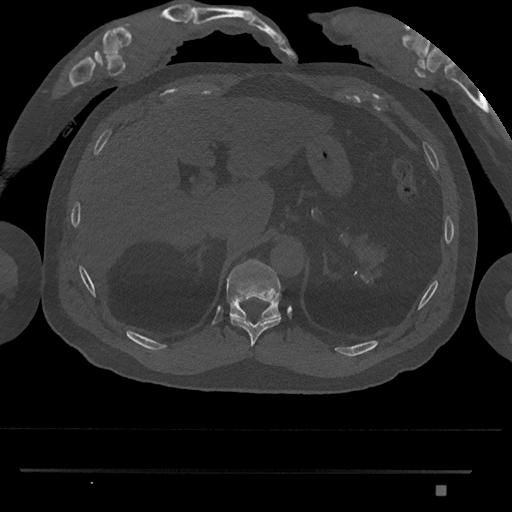
CT including the spine, one axial slice; slice 976 of 1134 in the series (ordered by position); 120 kVp; bone window (W 1800 / L 400 HU); 0.5 mm slice thickness; 512 × 512 image matrix, field of view 429 × 429 mm. Male patient, age 65 years. Case-level facts recorded for this patient, not image findings: primary cancer: prostate.
Structures marked on this image (semi-automatically segmented with operator editing):
- T10 vertebra: bounding box (x1, y1, x2, y2) in pixels: (230, 317, 281, 347)
- T11 vertebra: (226, 259, 281, 319)